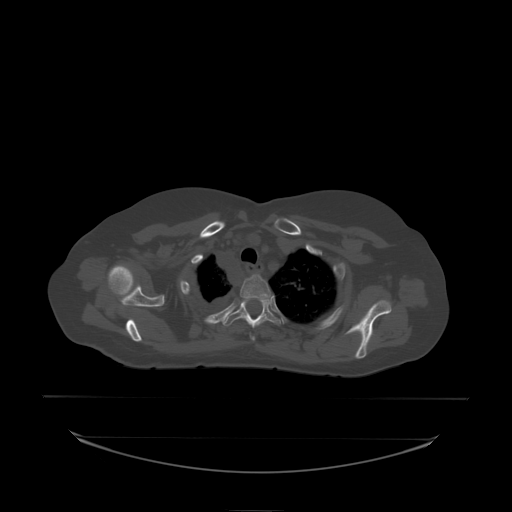
CT including the spine, one axial slice. Slice 176 of 242 in the series (ordered by position). Bone window (W 1800 / L 400 HU). 512 × 512 image matrix, field of view 500 × 500 mm. Patient: female, 53 years. From the clinical record (not read from this slice): primary cancer: lung.
Annotated regions visible in this slice (semi-automatic segmentation, software-assisted and operator-edited):
- T2 vertebra: bounding box <240,275,271,338> (left, top, right, bottom; pixels)
- T3 vertebra: <223,300,281,328>